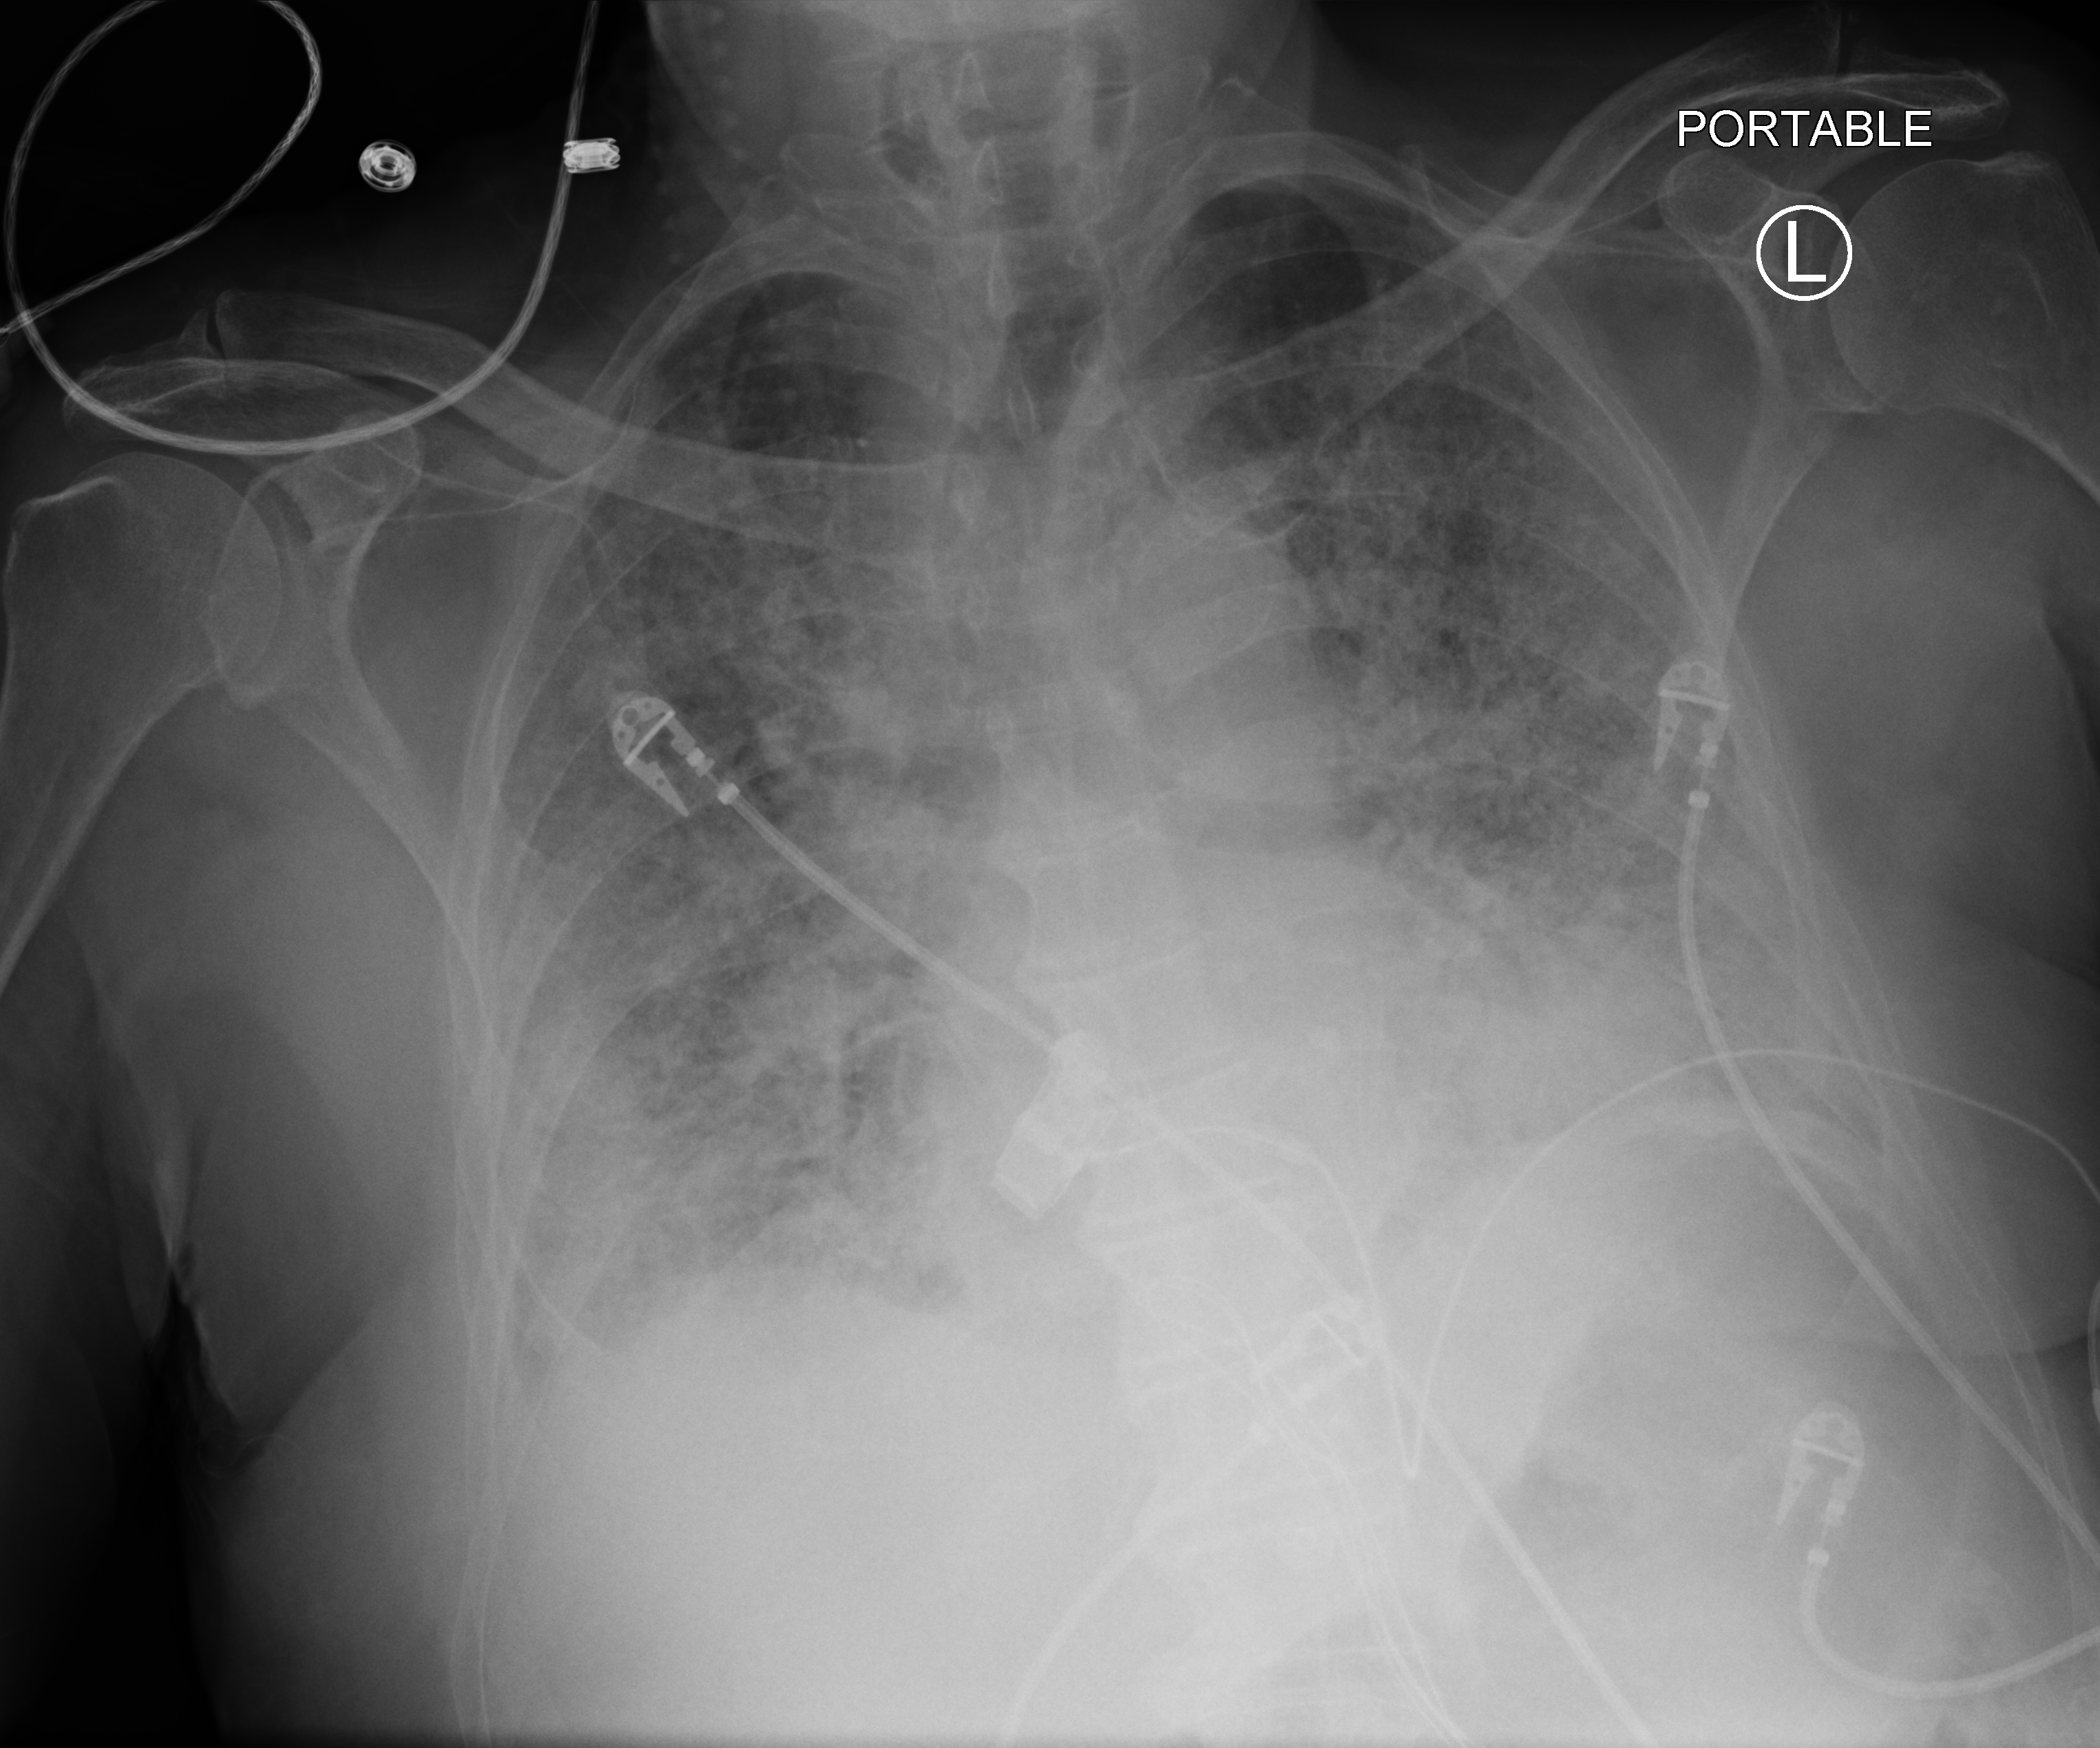
Chest X-ray (portable); anteroposterior (AP) projection. Male patient hospitalised with COVID-19, age 75–90 years.
Admission-level facts for this patient (not findings on this image; timing relative to this image not recorded): hypertension (admission record): no; admitted to intensive care during this hospital stay: yes.